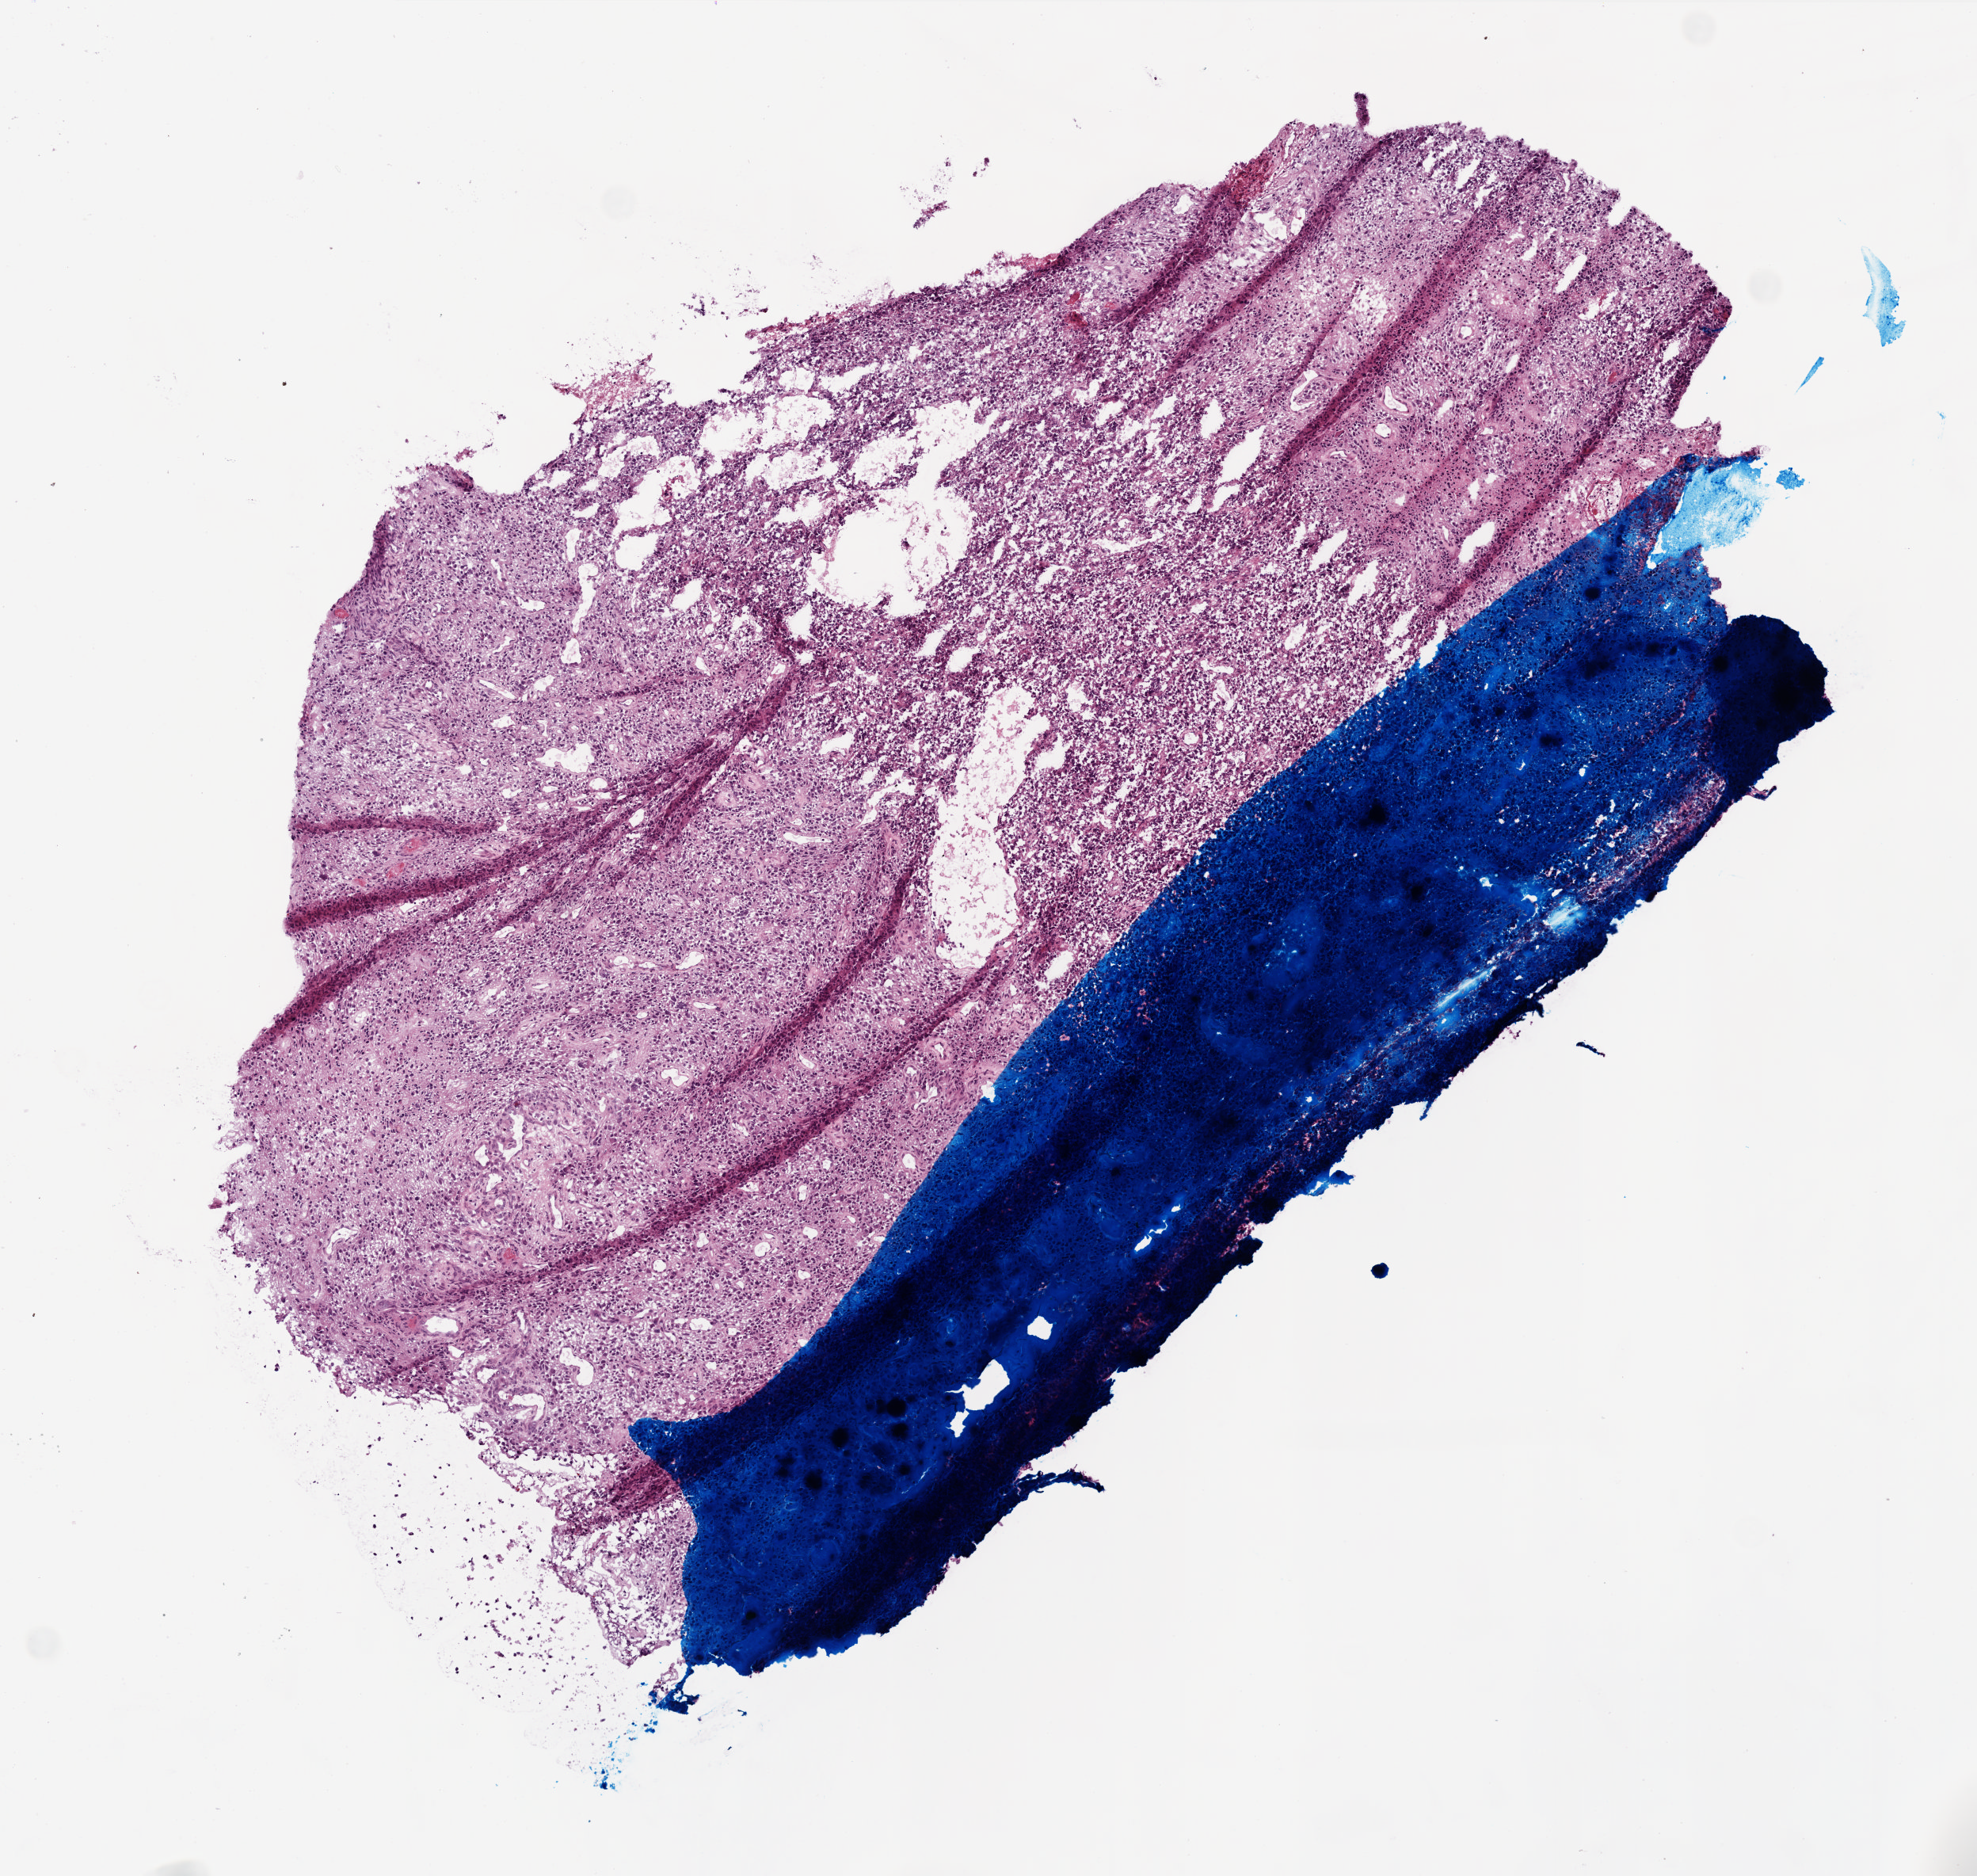
H&E-stained whole-slide image — shown as a low-resolution overview of the whole scanned area (about 5.0 x 4.7 mm, acquisition: 20x scan), frozen section, brain, primary tumour sample. Female patient; age at initial diagnosis 69 years. Composition of this section per pathologist review: tumour cells 95%, tumour nuclei 100%, normal cells 0%, stromal cells 0%, necrosis 5%.
Diagnosis: Glioblastoma.